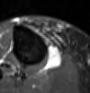
MRI of an extremity soft-tissue mass, one axial slice. STIR. MR volume resampled by the dataset authors to the PET/CT grid (not the native acquisition matrix). 3.27 mm slice thickness. 90 × 93 image matrix, field of view 88 × 91 mm. Female patient. From the clinical record (not read from this slice): histological type: undifferentiated – high grade; grade: high; site of the primary tumour: right thigh.
Outlined on this slice (expert contour drawn on MRI and transferred to this co-registered scan by the dataset authors):
- gross tumour volume (mass): bounding box <46,46,63,70> (left, top, right, bottom; pixels)